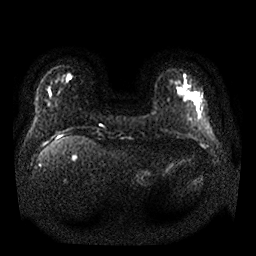
Breast MRI, one axial slice. Slice 4 of 25 in the series (ordered by position). Diffusion-weighted series; image 2 of 4 stored at this slice position (different b-values; order by instance number). 1.5 T. 256 × 256 image matrix, field of view 340 × 340 mm. Female patient.
Annotated regions visible in this slice (expert manual segmentation):
- tumour on diffusion-weighted imaging: bounding box <185,93,200,112> (left, top, right, bottom; pixels)